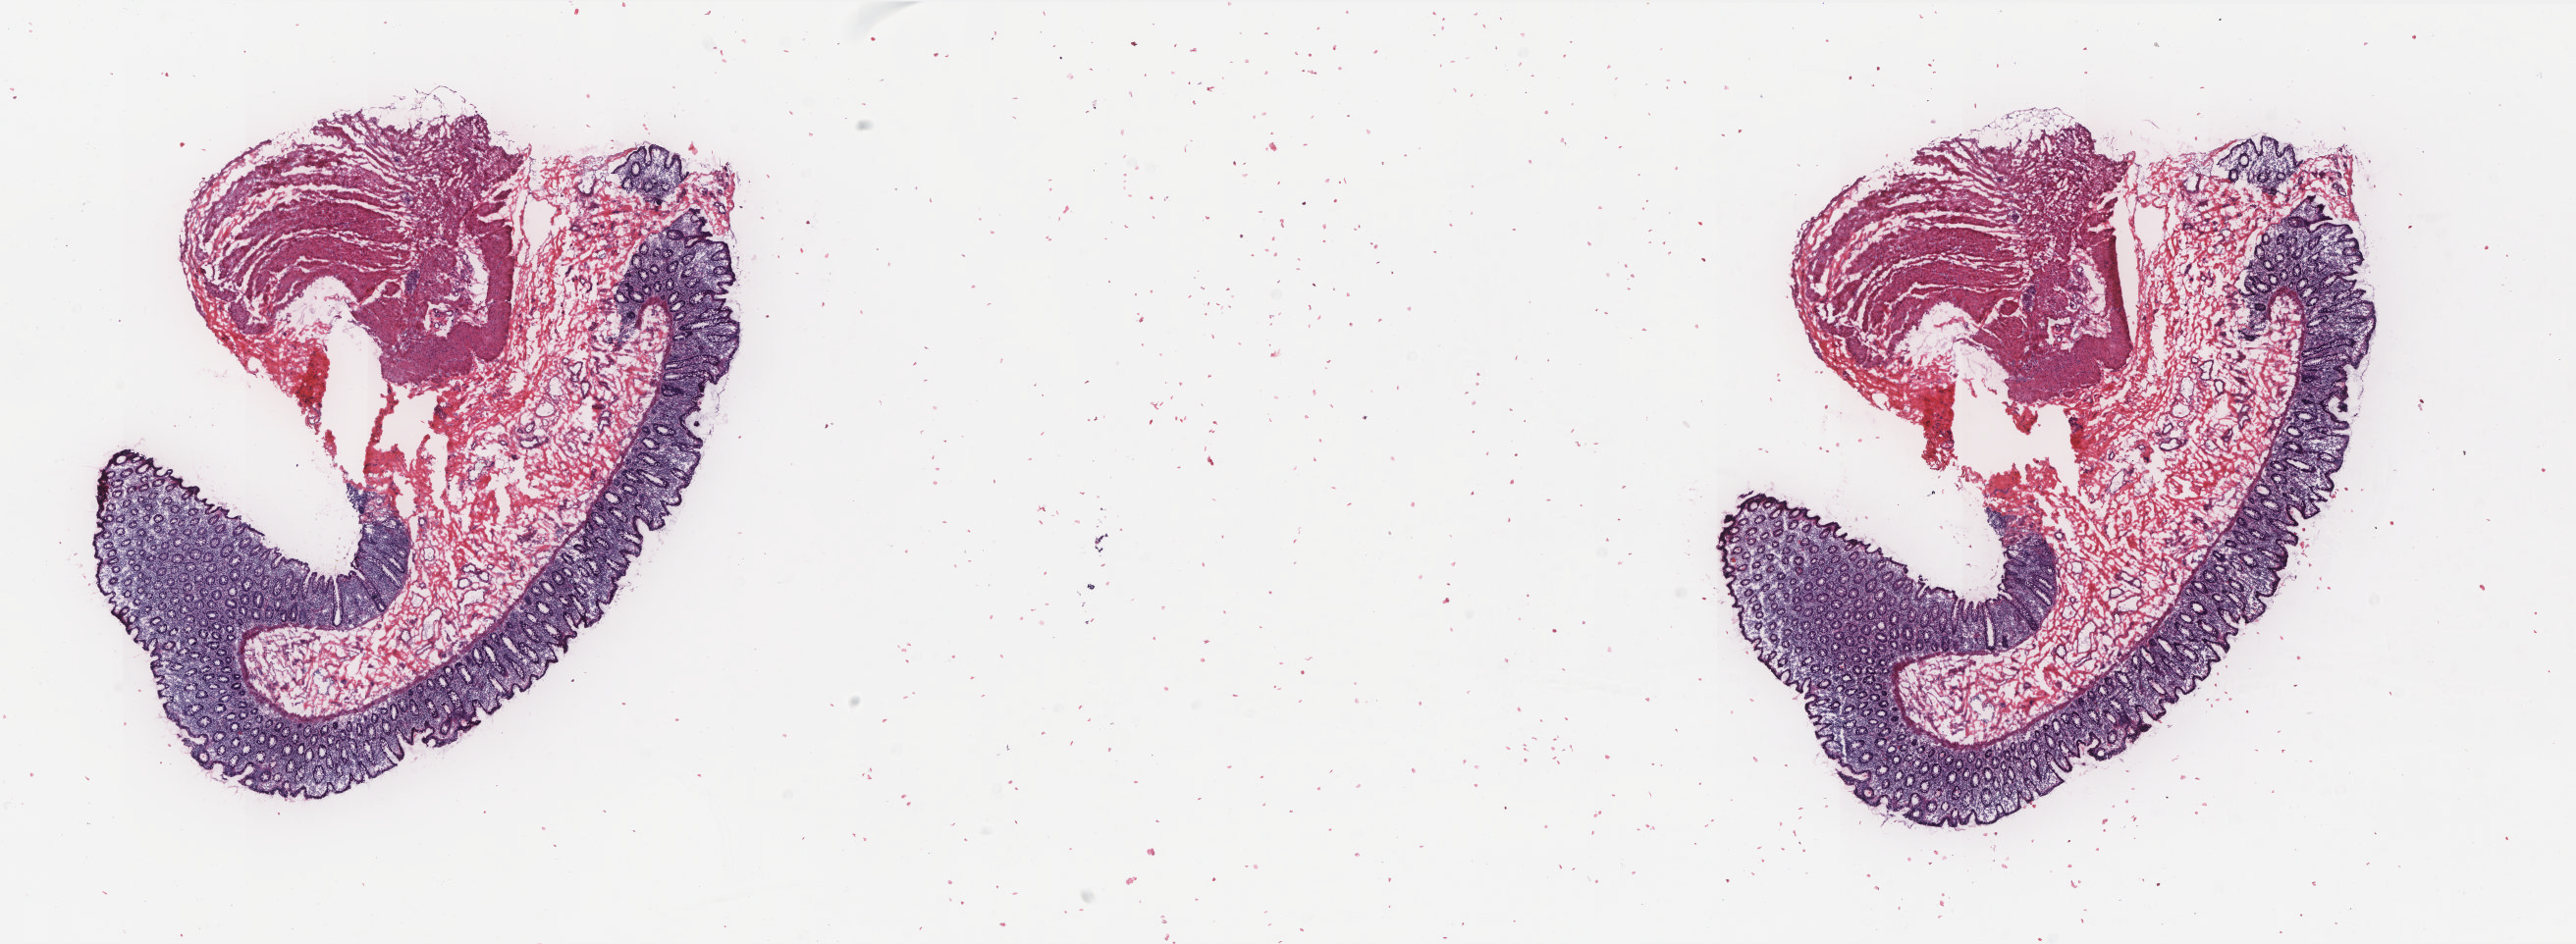
Whole-slide histology image, Hematoxylin and eosin (H&E) stained — low-resolution overview of the scanned area, about 21.0 x 7.7 mm; frozen section from the top of the tissue portion; solid tissue normal (non-tumour tissue) sample from the colon. Female patient. Slide review estimates, as recorded: tumour cells 0%, normal cells 100%. Inflammatory infiltration, as recorded: lymphocyte infiltration 40%, monocyte infiltration 10%, neutrophil infiltration 0%.
• this section: solid tissue normal sample (biorepository sample class)
• patient diagnosis: Mucinous adenocarcinoma (cecum)